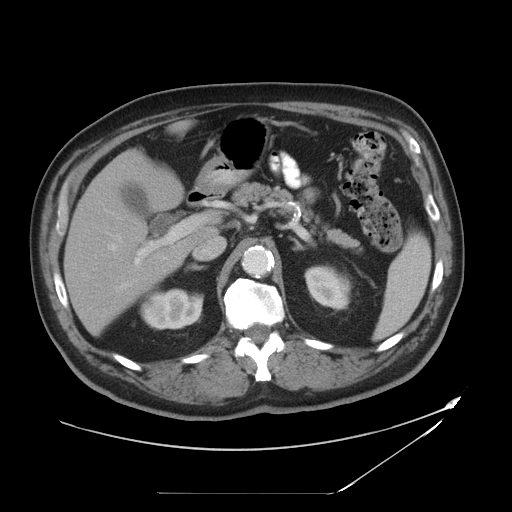
Contrast-enhanced abdominal CT, one axial slice; slice 26 of 49 in the series (ordered by position); reconstruction kernel STANDARD; 120 kVp; soft-tissue window (W 400 / L 40 HU); 5 mm slice thickness; 512 × 512 image matrix, field of view 461 × 461 mm. Male patient, age 72 years. From the clinical record (not read from this slice): diagnosis: colorectal cancer liver metastases, imaged before liver resection; multiple liver metastases: no; largest metastasis: 2.5 cm; disease in both lobes: no.
Annotated regions visible in this slice (outlined manually by an expert reader):
- hepatic veins: box from (x=107, y=232) to (x=123, y=252) px
- liver: (x=65, y=155)–(x=209, y=333)
- planned liver remnant (the part of the liver to remain after resection): (x=65, y=164)–(x=187, y=333)
- portal vein (with intrahepatic branches): (x=134, y=216)–(x=208, y=282)